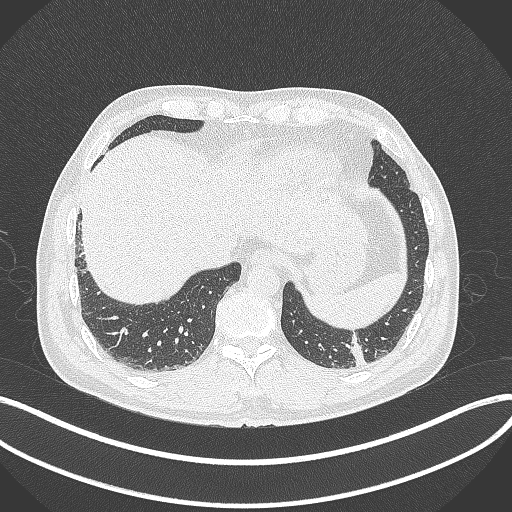
Chest CT, one axial slice. Slice 52 of 300 in the series (ordered by position). 120 kVp. Lung window (W 1500 / L -600 HU). 512 × 512 image matrix, field of view 400 × 400 mm. Patient: male, 54 years. From the clinical record (not read from this slice): clinical TNM (as recorded): T1c N0 M1; histopathological grade: G3.
Outlined on this slice (bounding box drawn by a radiologist):
- lung tumour (recorded histology: adenocarcinoma): bounding box [x1, y1, x2, y2] px = [347, 332, 365, 368]